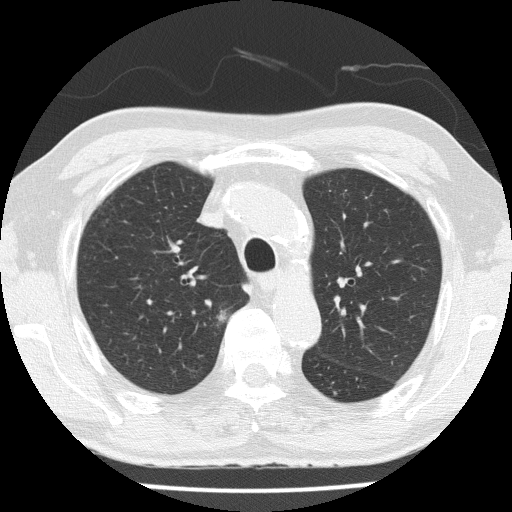
Axial slice from a low-dose chest CT screening exam, third screening round (two years after baseline), lung window (W 1500 / L -600 HU), lung (sharp) reconstruction kernel (FC51), 120 kVp. Male participant, aged 72 years at enrolment. Current smoker at enrolment.
Lesion marked by an expert reader, box from (x=187, y=292) to (x=243, y=347) px. Reader record for this screening exam (exam-level; its link to the box is not recorded): non-calcified nodule or mass ≥4 mm, right upper lobe, 14 × 14 mm, spiculated (stellate) margins, soft tissue attenuation, pre-existing on the prior screen: yes; interval growth: yes.